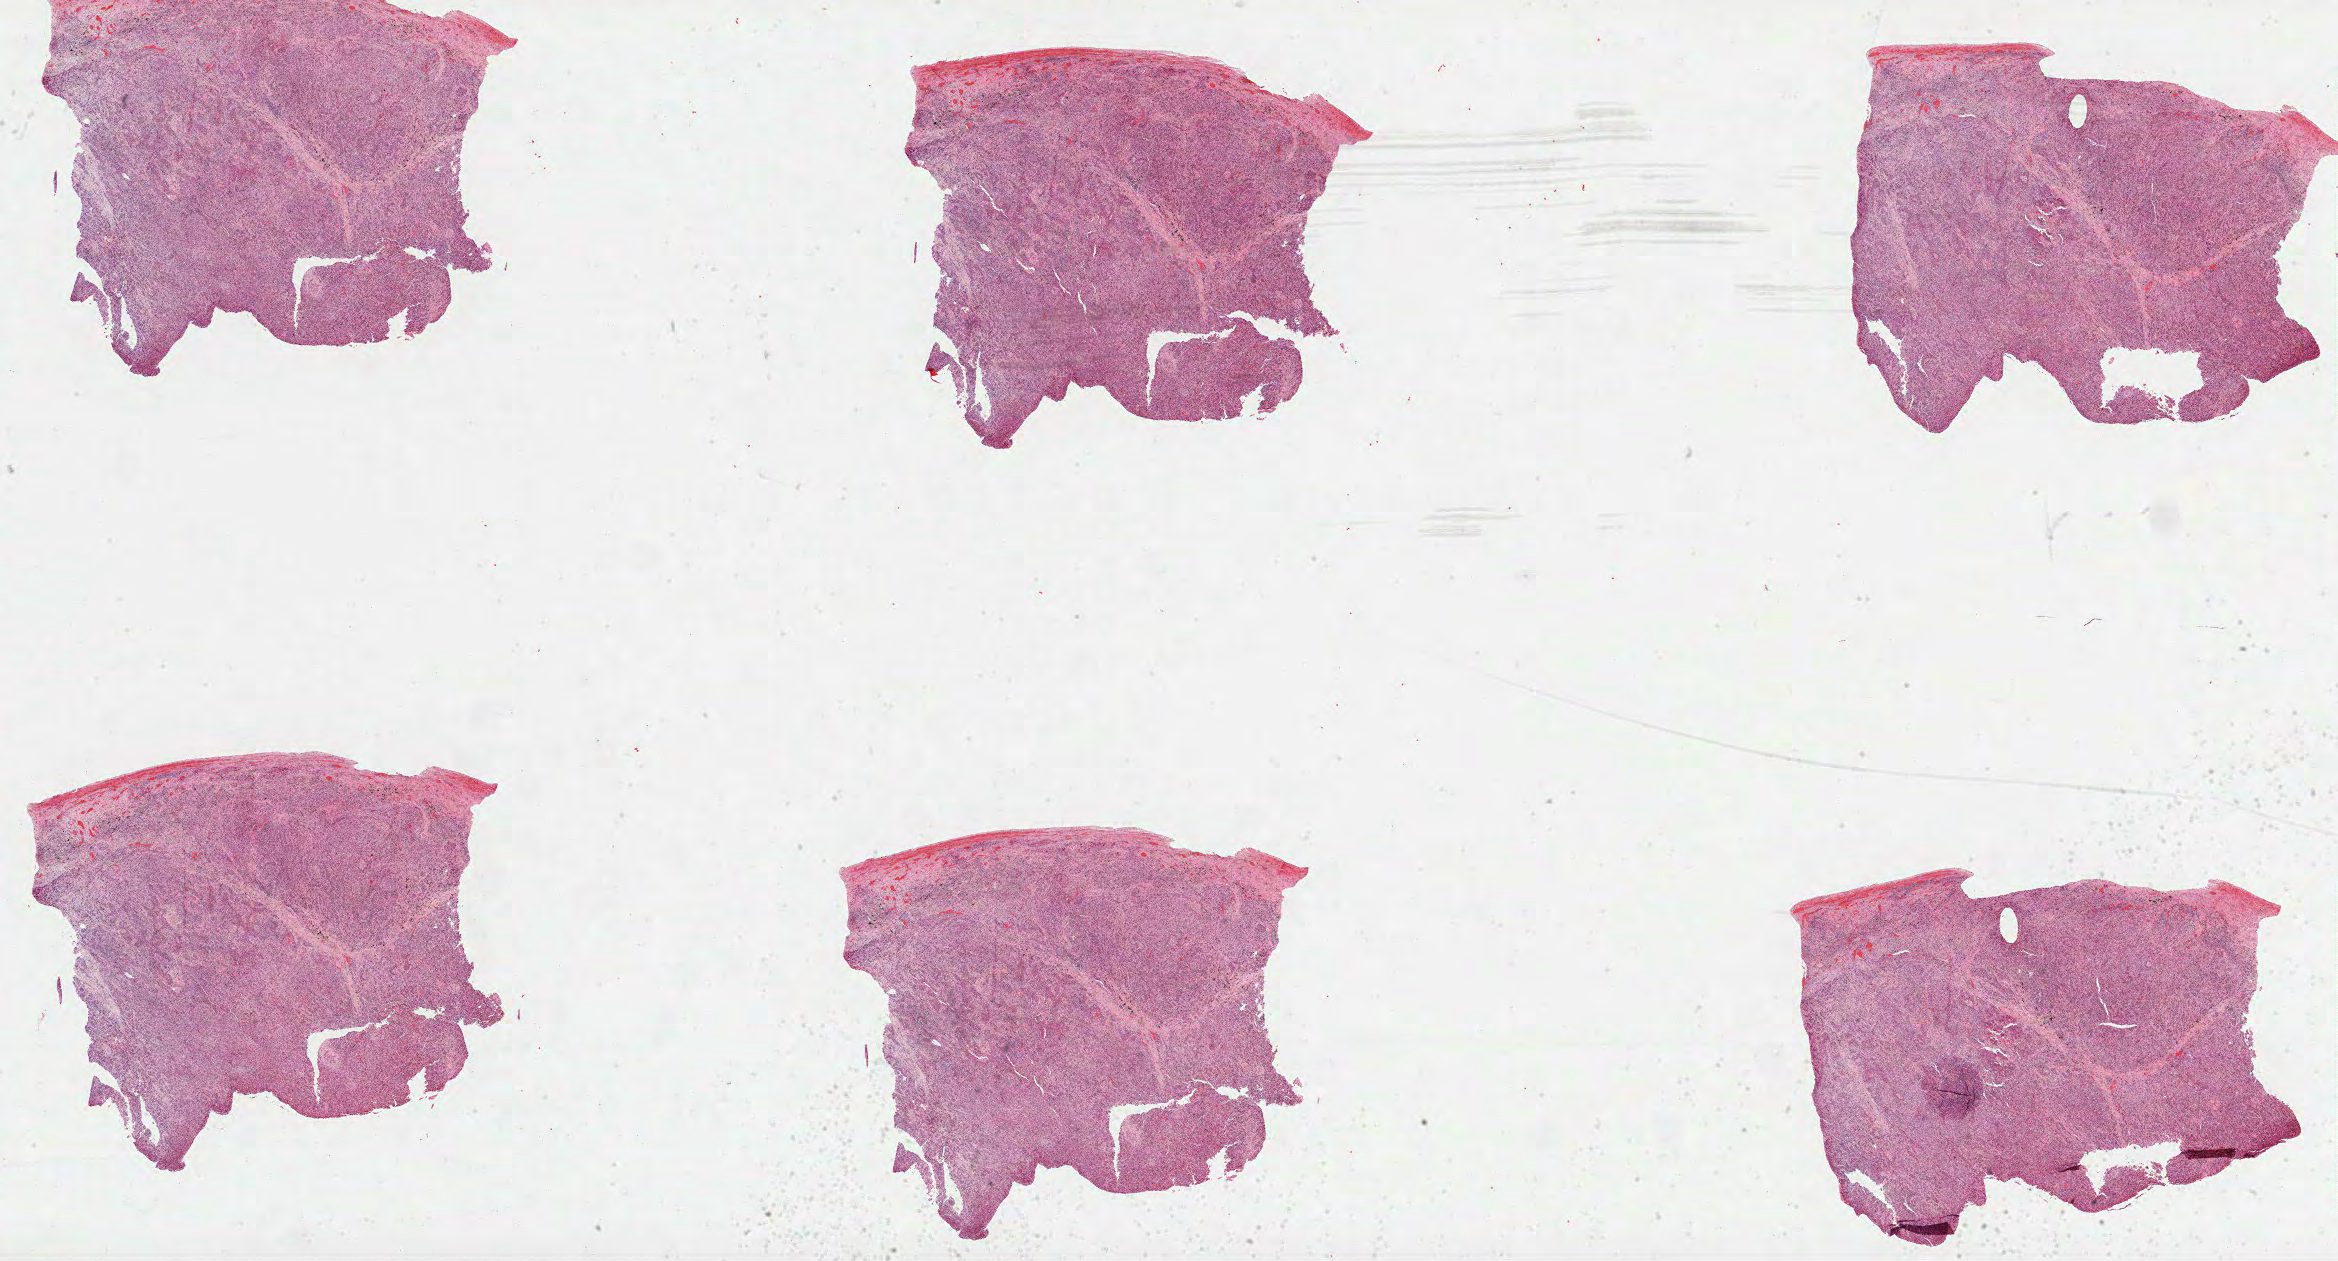
Whole-slide histology image, H&E-stained, shown as a low-resolution overview of the whole scanned area (about 37.7 x 20.3 mm, from a 40x scan). FFPE section. Primary tumour sample from the lung. Male patient; age at initial diagnosis 57 years.
• pathologic diagnosis: Squamous cell carcinoma, NOS (upper lobe, lung)
• laterality: right